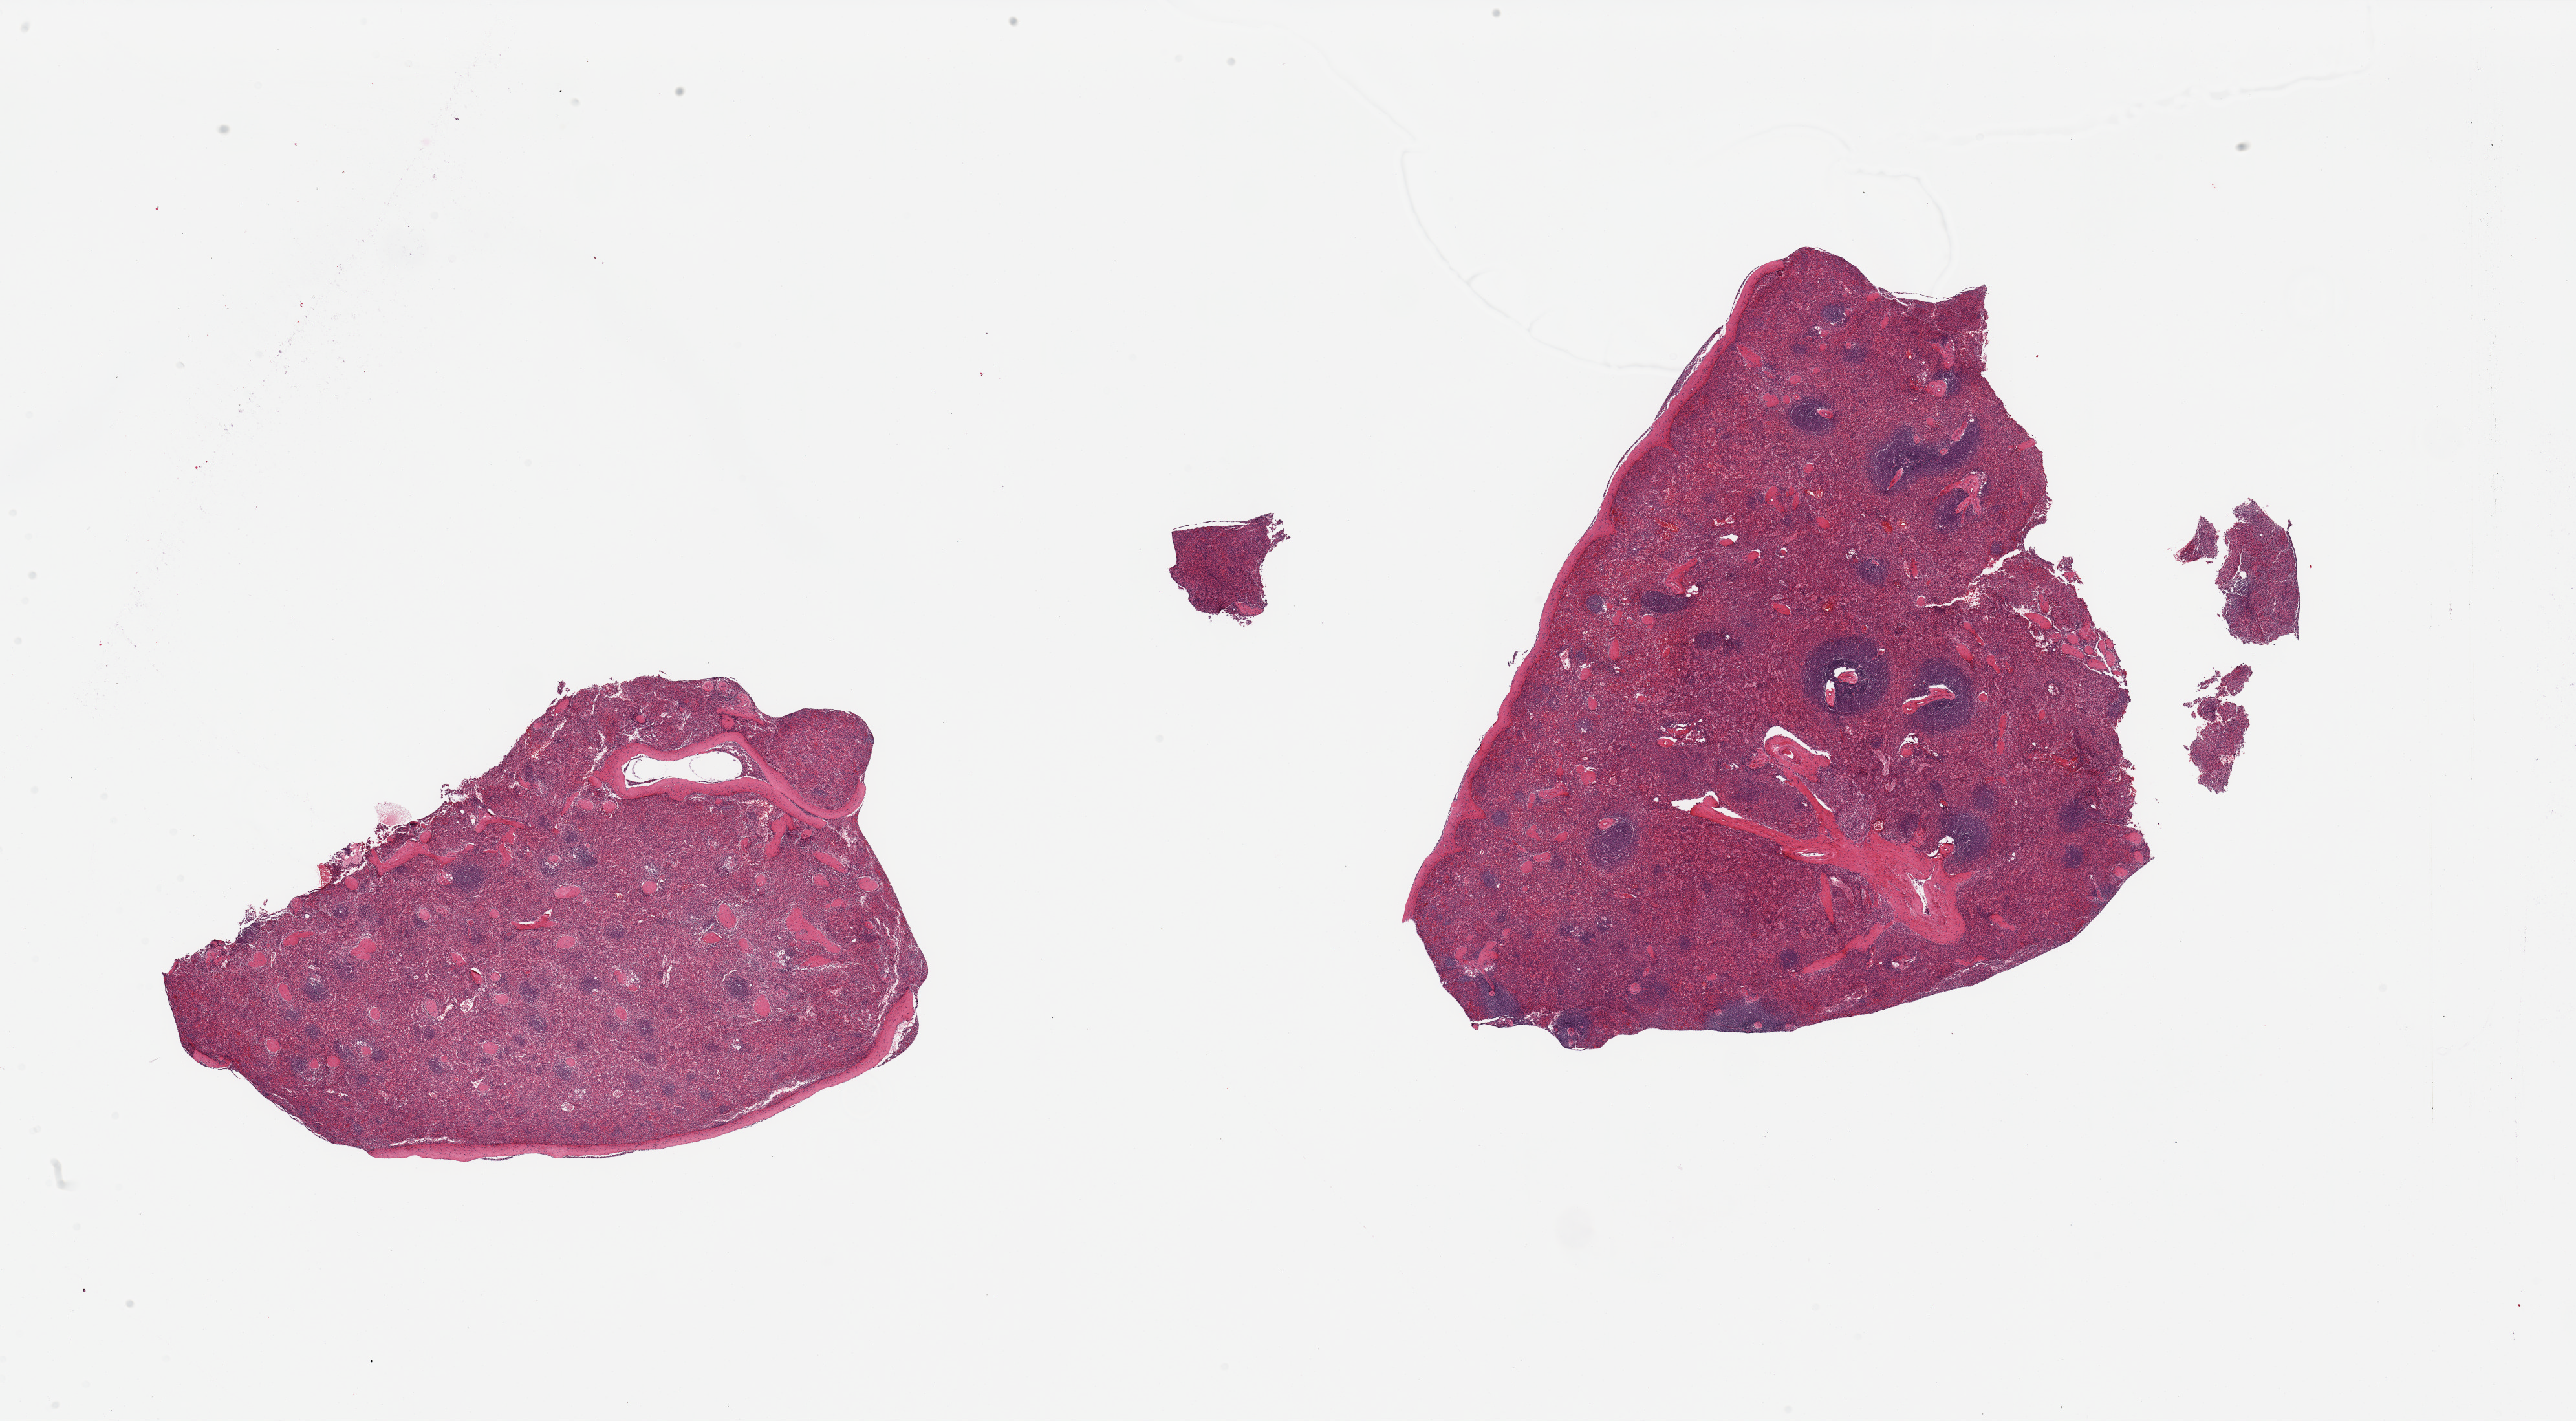
Digitized hematoxylin and eosin (H&E)-stained section, low-resolution overview of the scanned area, about 31.5 x 17.4 mm, PAXgene-fixed paraffin-embedded (PFPE) section, target tissue: spleen, donor tissue sample. Donor sex: female.
Reviewer comment on this tissue sample: 2 pieces, no abnormalities.